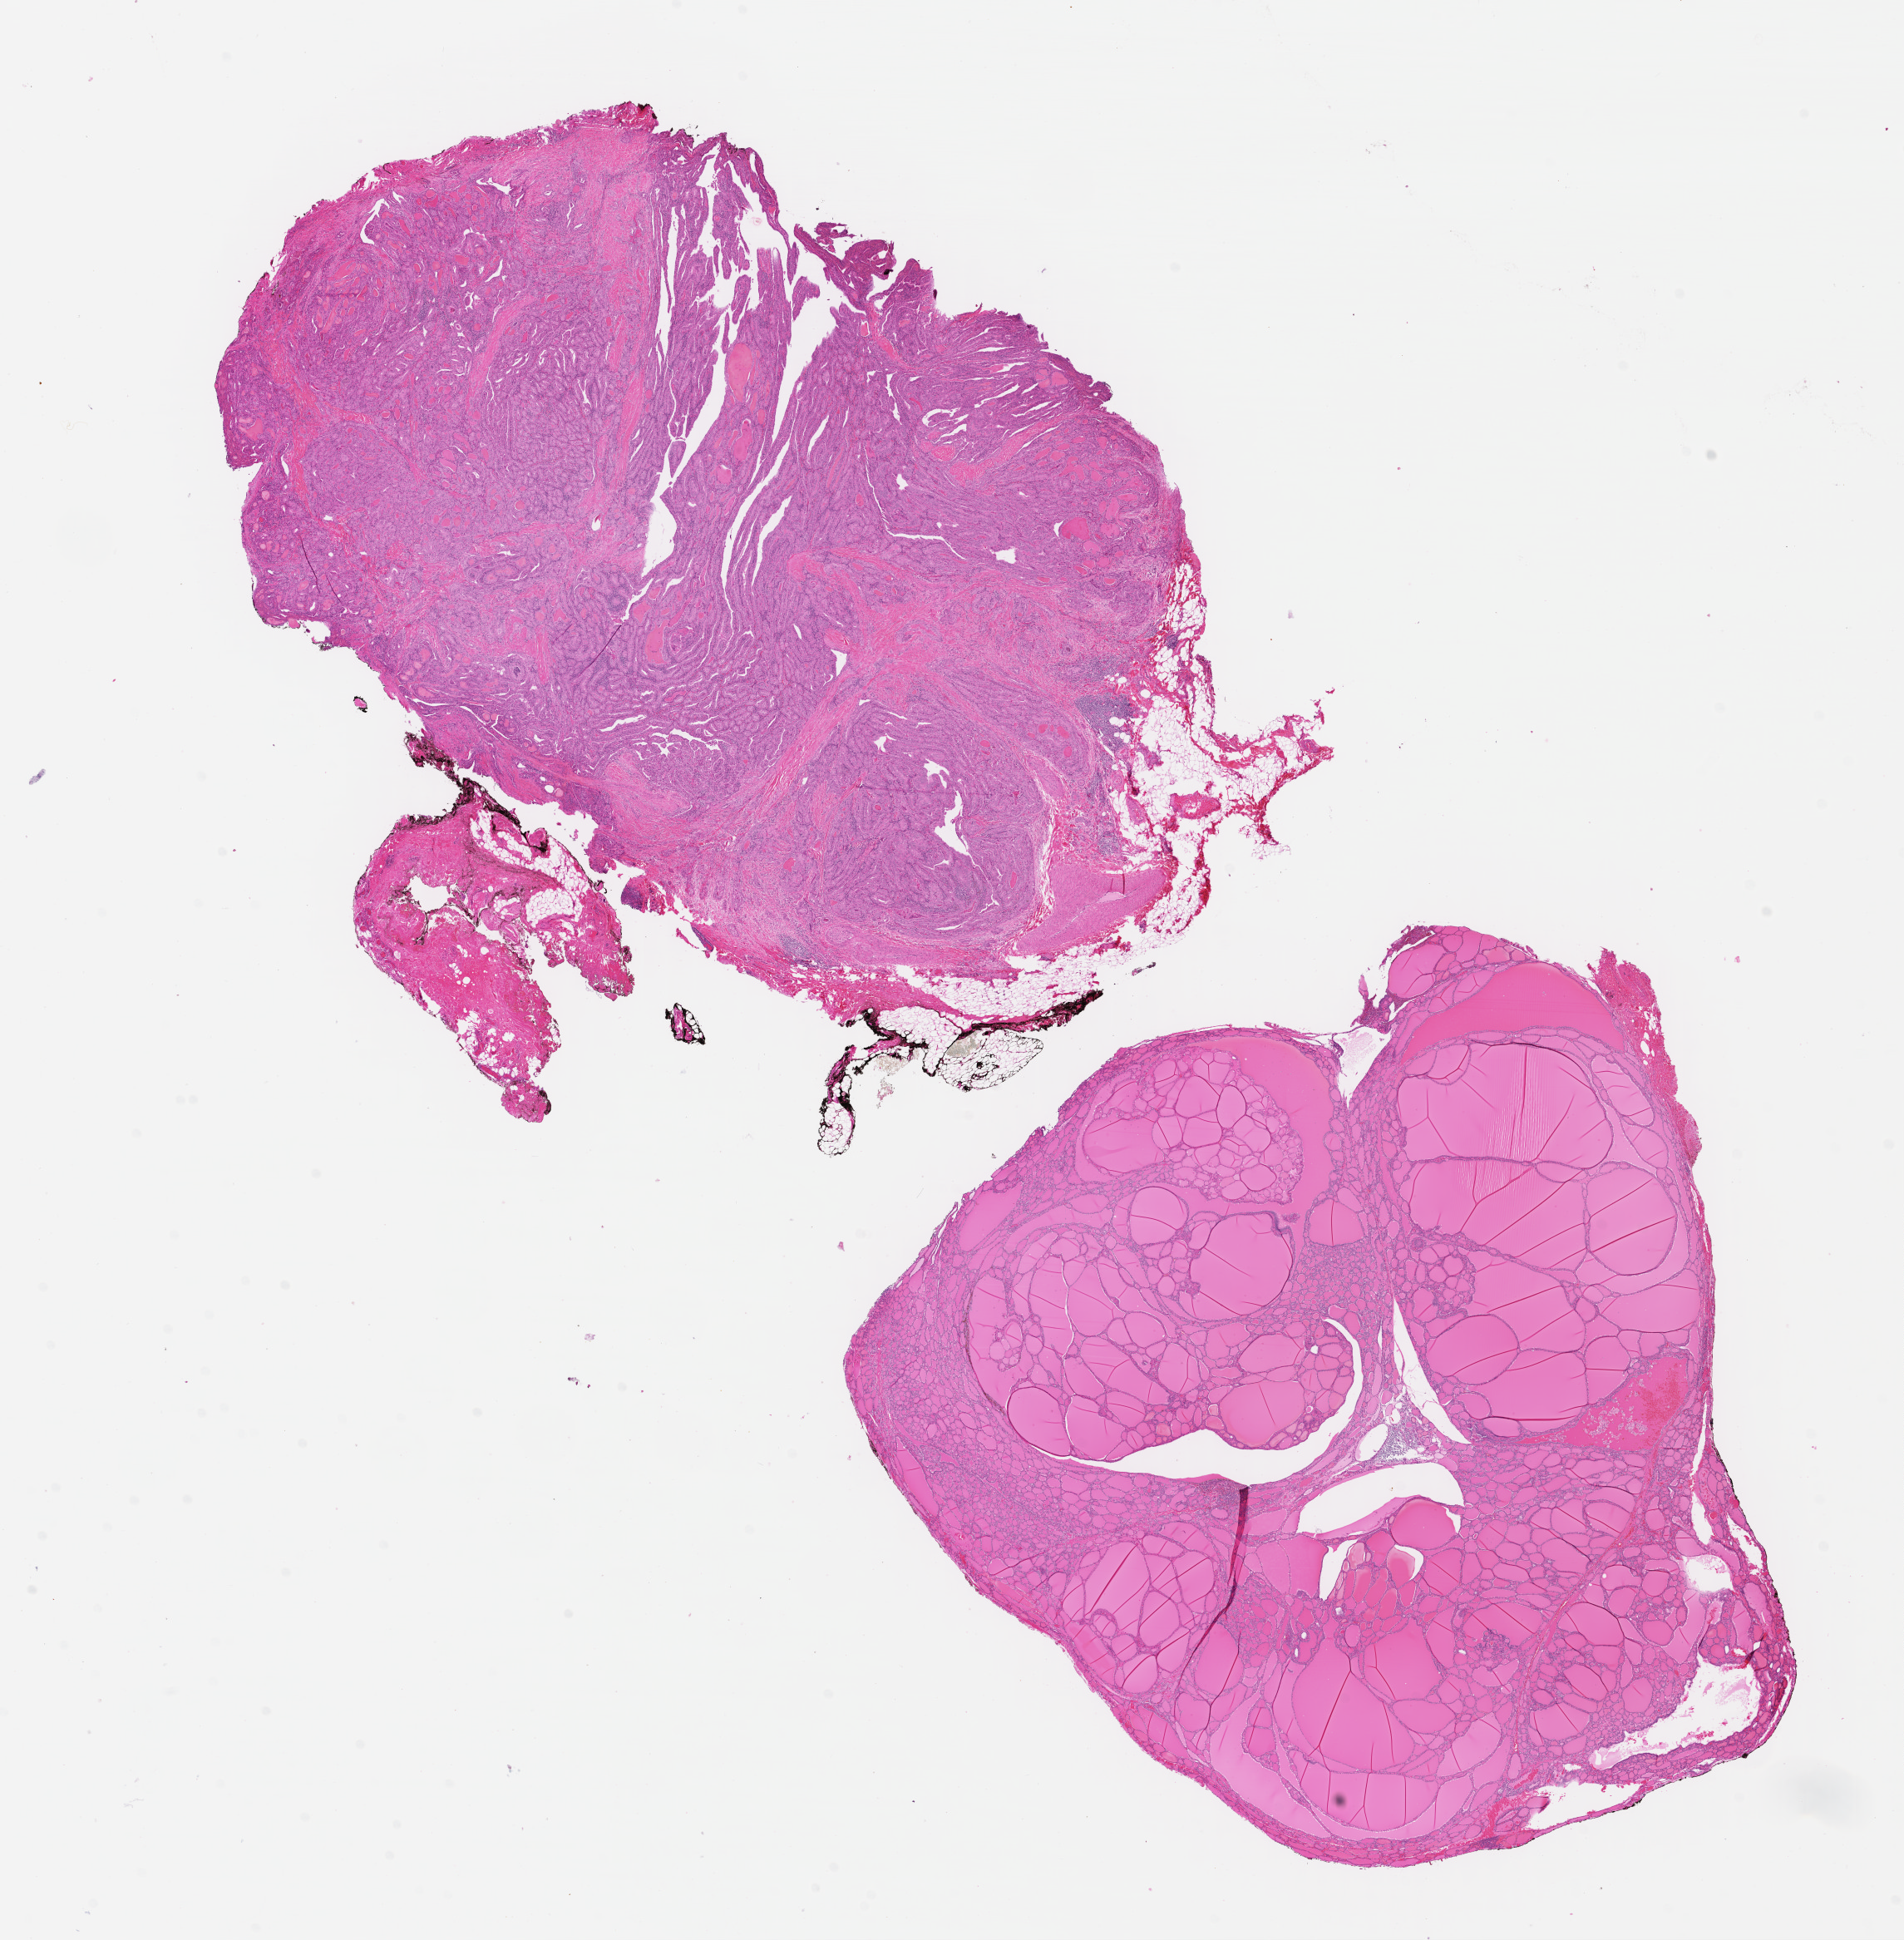
H&E-stained whole-slide image — whole scanned area (about 18.0 x 18.3 mm) shown as a low-resolution overview; FFPE section; thyroid, primary tumour sample. Female patient; age at initial diagnosis 53 years.
• TNM: T3 NX M0
• laterality: left
• AJCC pathologic stage: II (5th edition)
• pathologic diagnosis: Papillary adenocarcinoma, NOS (thyroid gland)